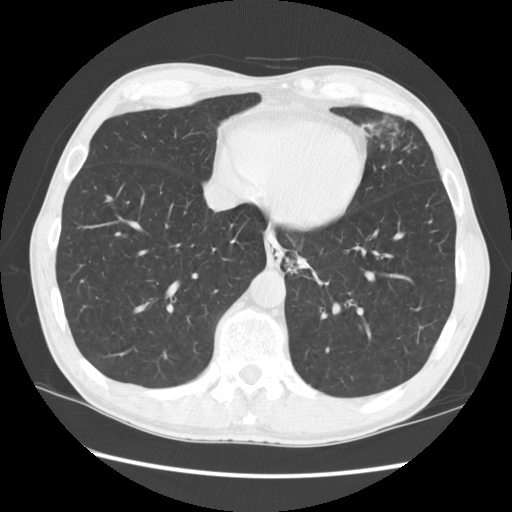
Chest CT (low-dose screening protocol), one axial image, first (baseline) screen, lung window (W 1500 / L -600 HU), 2.5 mm slice thickness, standard (soft-tissue) reconstruction kernel (STANDARD), slice 104 of 141 in the series, 512 × 512 image matrix, field of view 360 × 360 mm. Male, age 57 years at enrolment. Current smoker at enrolment.
Expert-annotated lung lesion, box from (x=270, y=239) to (x=335, y=299) px. The screening reader recorded 2 non-calcified nodules or masses ≥4 mm on this exam (left lower lobe, lingula); which of them this box marks is not recorded. Official screen result: positive, change unspecified: nodule(s) >= 4 mm or enlarging nodule(s), mass(es), or other non-specific abnormalities suspicious for lung cancer. Later outcome: lung cancer diagnosed 95 days after this screen — squamous cell carcinoma, NOS, left lower lobe, moderately differentiated (G2), stage IB (AJCC 6th edition), 35 mm at pathology.